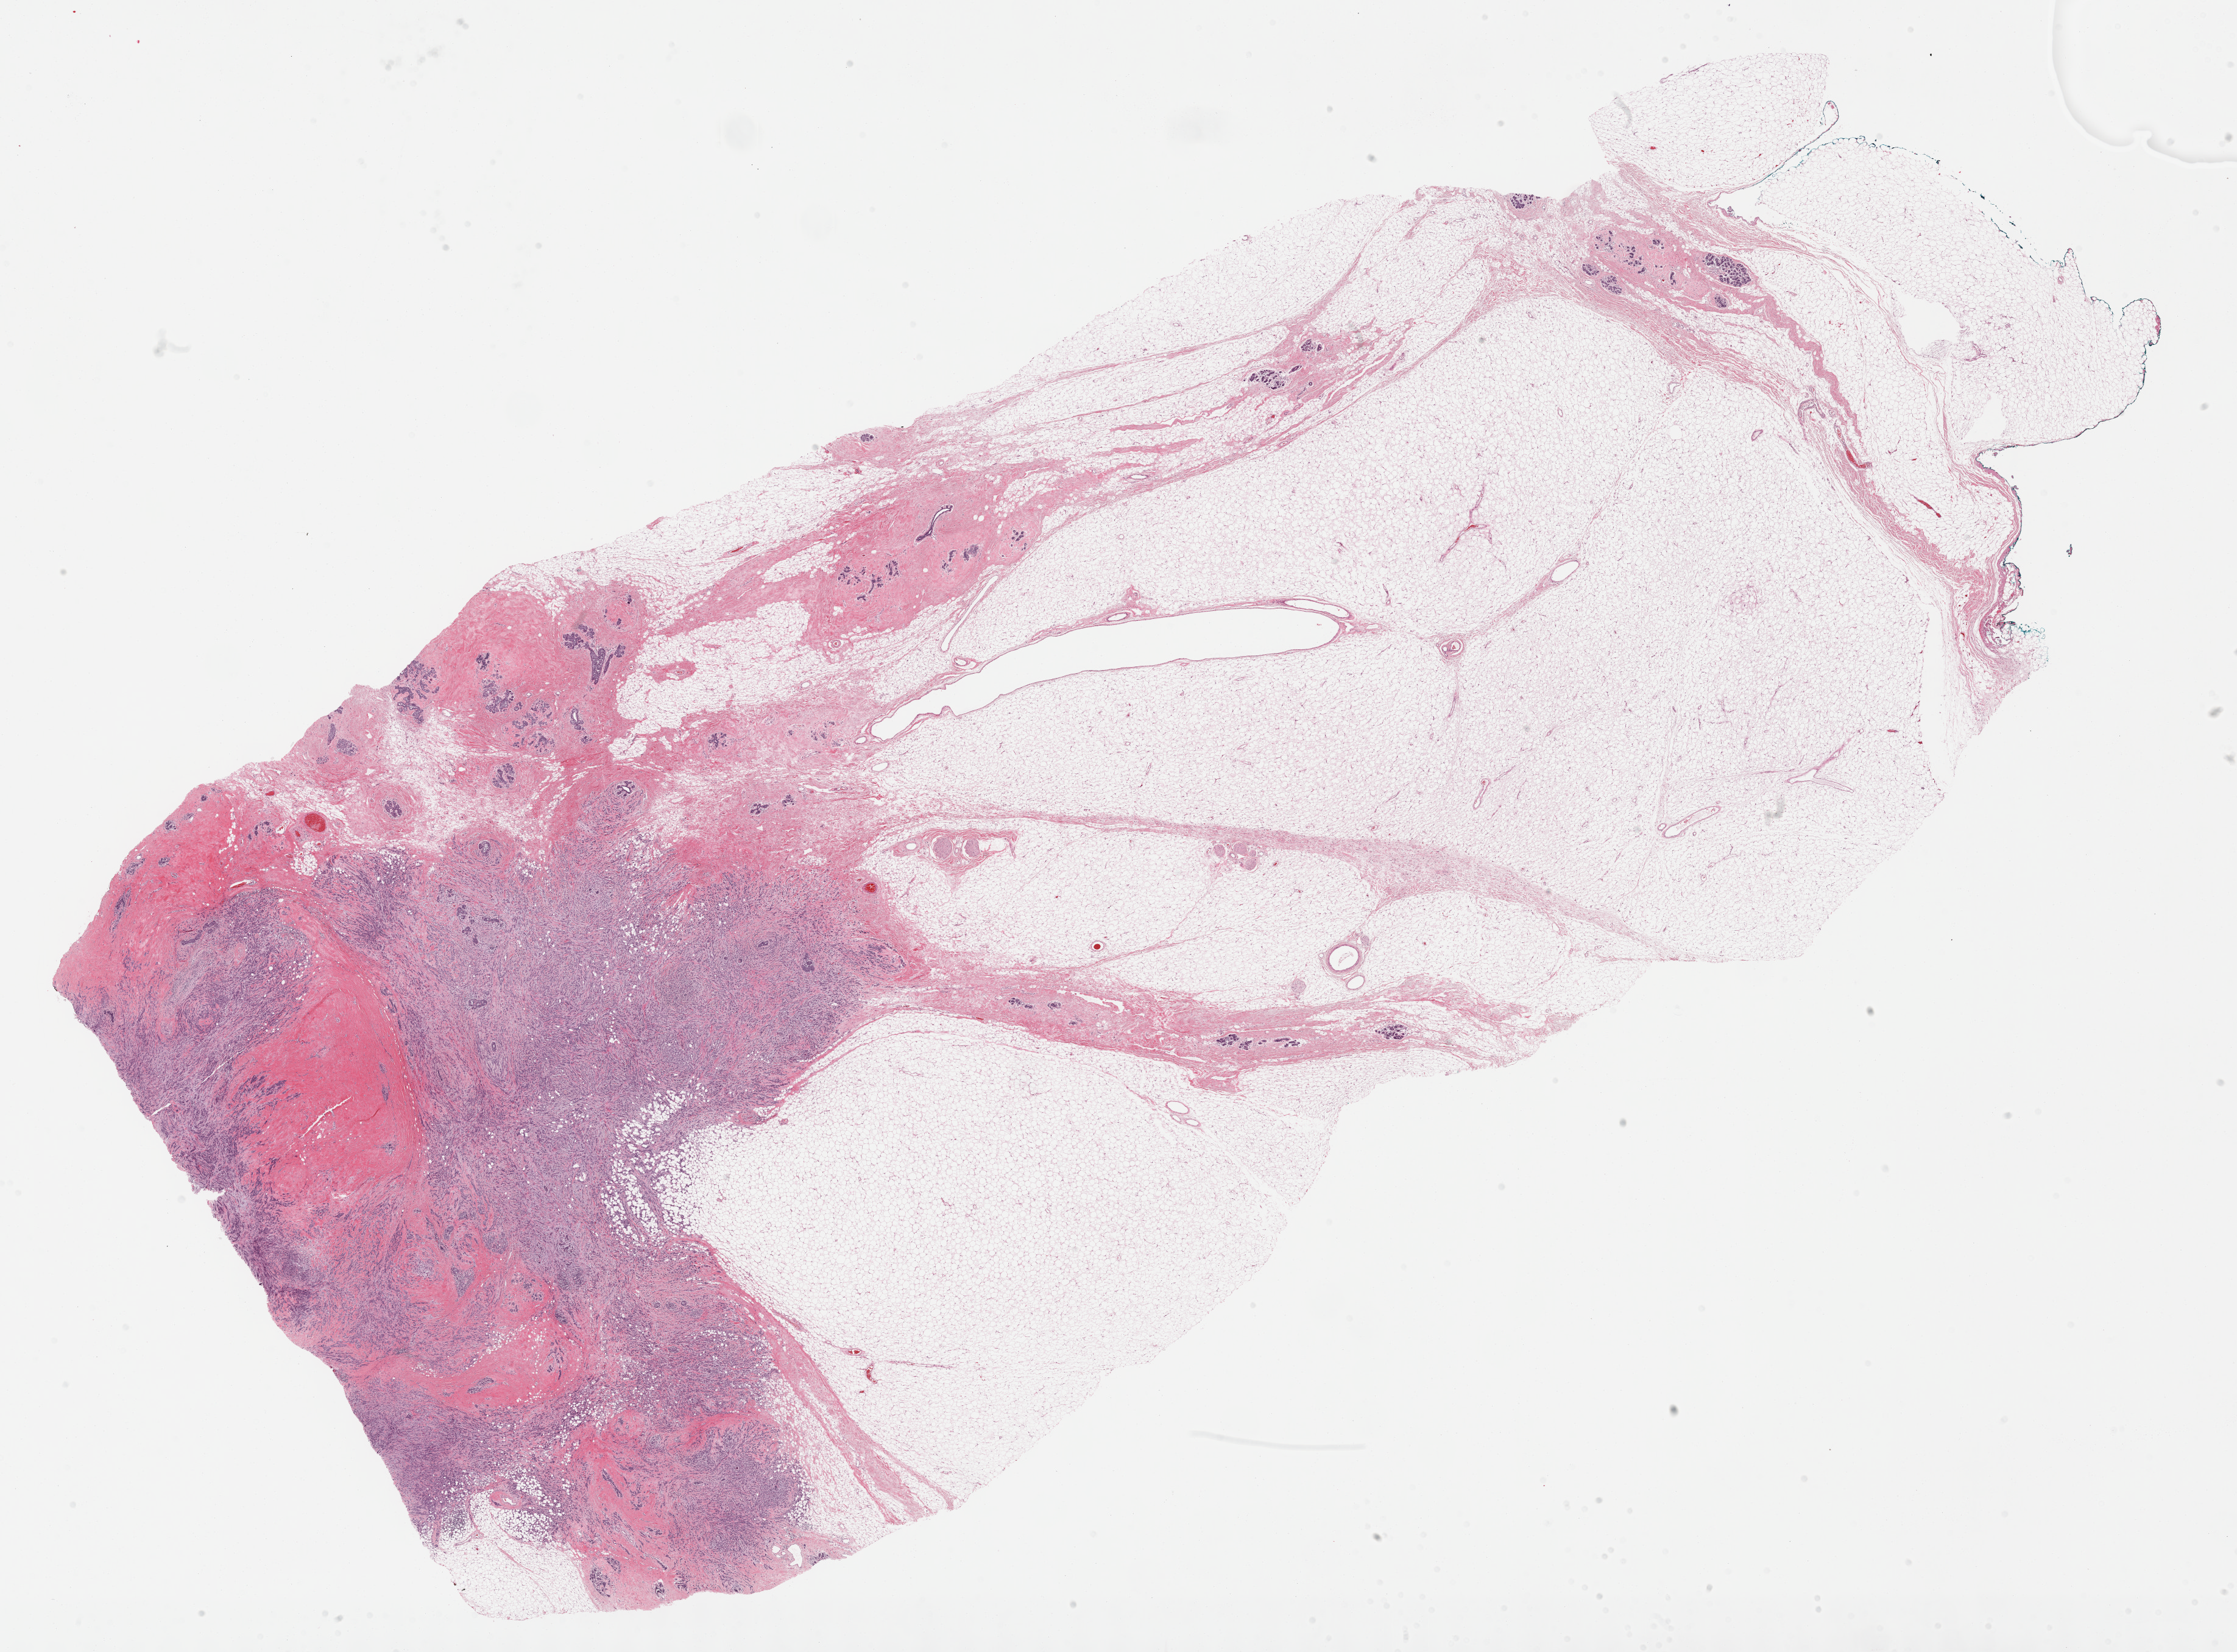
H&E-stained whole-slide image, a low-resolution overview of the entire scanned area, about 29.7 x 21.9 mm; formalin-fixed paraffin-embedded (FFPE) diagnostic section; breast, primary tumour sample. Female patient; age at initial diagnosis 46 years.
Diagnosis: Lobular carcinoma, NOS. AJCC pathologic stage: IIIA.